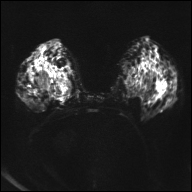
Breast MRI, one axial slice. Slice 17 of 32 in the series (ordered by position). Diffusion-weighted series; image 2 of 4 stored at this slice position (different b-values; order by instance number). 1.5 T. 4 mm slice thickness. 192 × 192 image matrix, field of view 360 × 360 mm. Female patient.
Annotated regions visible in this slice (outlined manually by an expert reader):
- tumour on diffusion-weighted imaging: bounding box <33,70,73,97> (left, top, right, bottom; pixels)